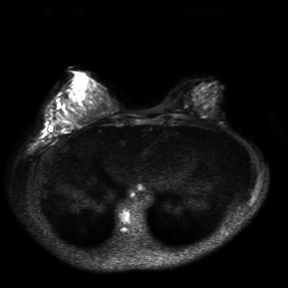
Breast MRI, one axial slice. Slice 11 of 30 in the series (ordered by position). Diffusion-weighted series; image 2 of 4 stored at this slice position (different b-values; order by instance number). 3 T. 4 mm slice thickness. 288 × 288 image matrix, field of view 360 × 360 mm. Female patient.
Outlined on this slice (outlined manually by an expert reader):
- tumour on diffusion-weighted imaging: bounding box [x1, y1, x2, y2] px = [60, 116, 64, 122]